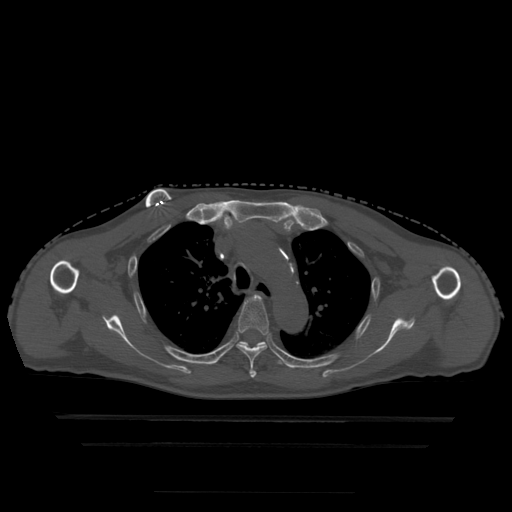
CT including the spine, one axial slice. Position 351 of 522 along the scan axis. Bone window (W 1800 / L 400 HU). 512 × 512 image matrix. Patient age 68 years. From the clinical record (not read from this slice): primary cancer: urothelial.
Annotated regions visible in this slice (semi-automatically segmented with operator editing):
- T4 vertebra: box from (x=237, y=296) to (x=270, y=379) px
- T5 vertebra: (x=240, y=342)–(x=283, y=366)